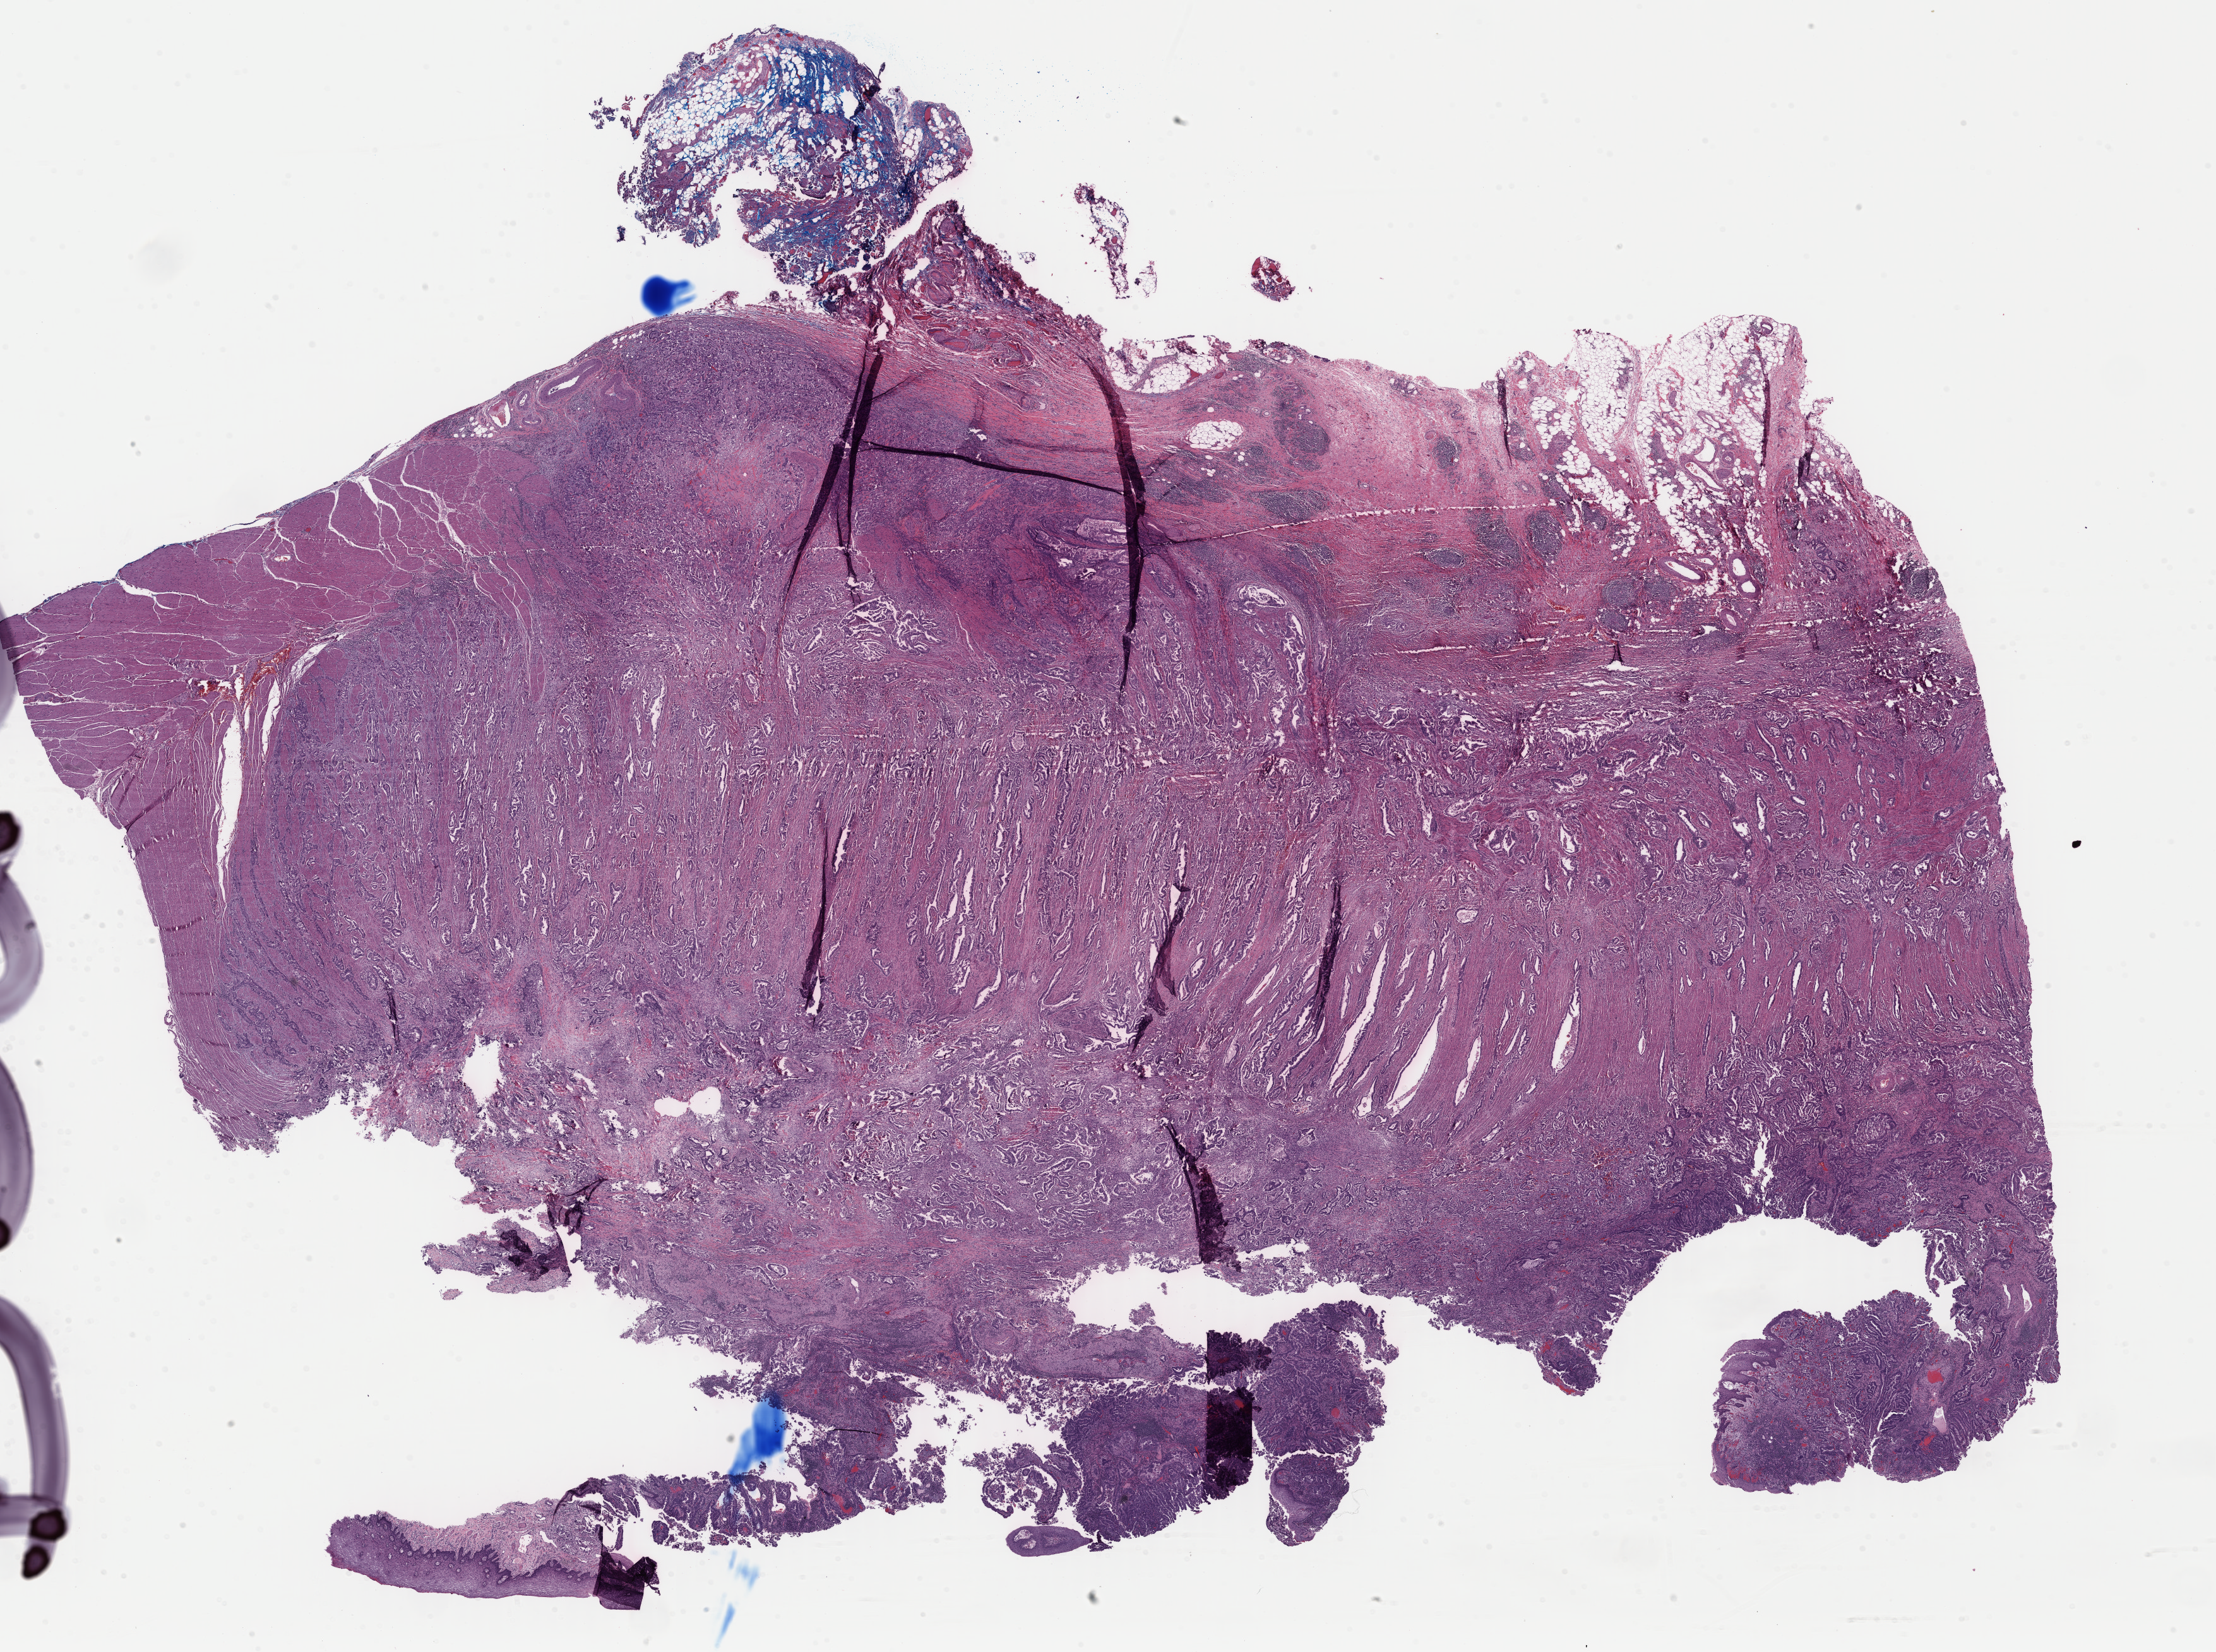
Whole-slide histology image, H&E-stained, whole scanned area (about 27.7 x 20.6 mm, slide scanned at 40x) shown as a low-resolution overview, FFPE section, sample: primary tumour, esophagus. Male patient; age at initial diagnosis 75 years. Histologic grade: G2 (moderately differentiated).
Diagnosis: Adenocarcinoma, NOS (lower third of esophagus). AJCC pathologic stage: IIIC (7th edition).